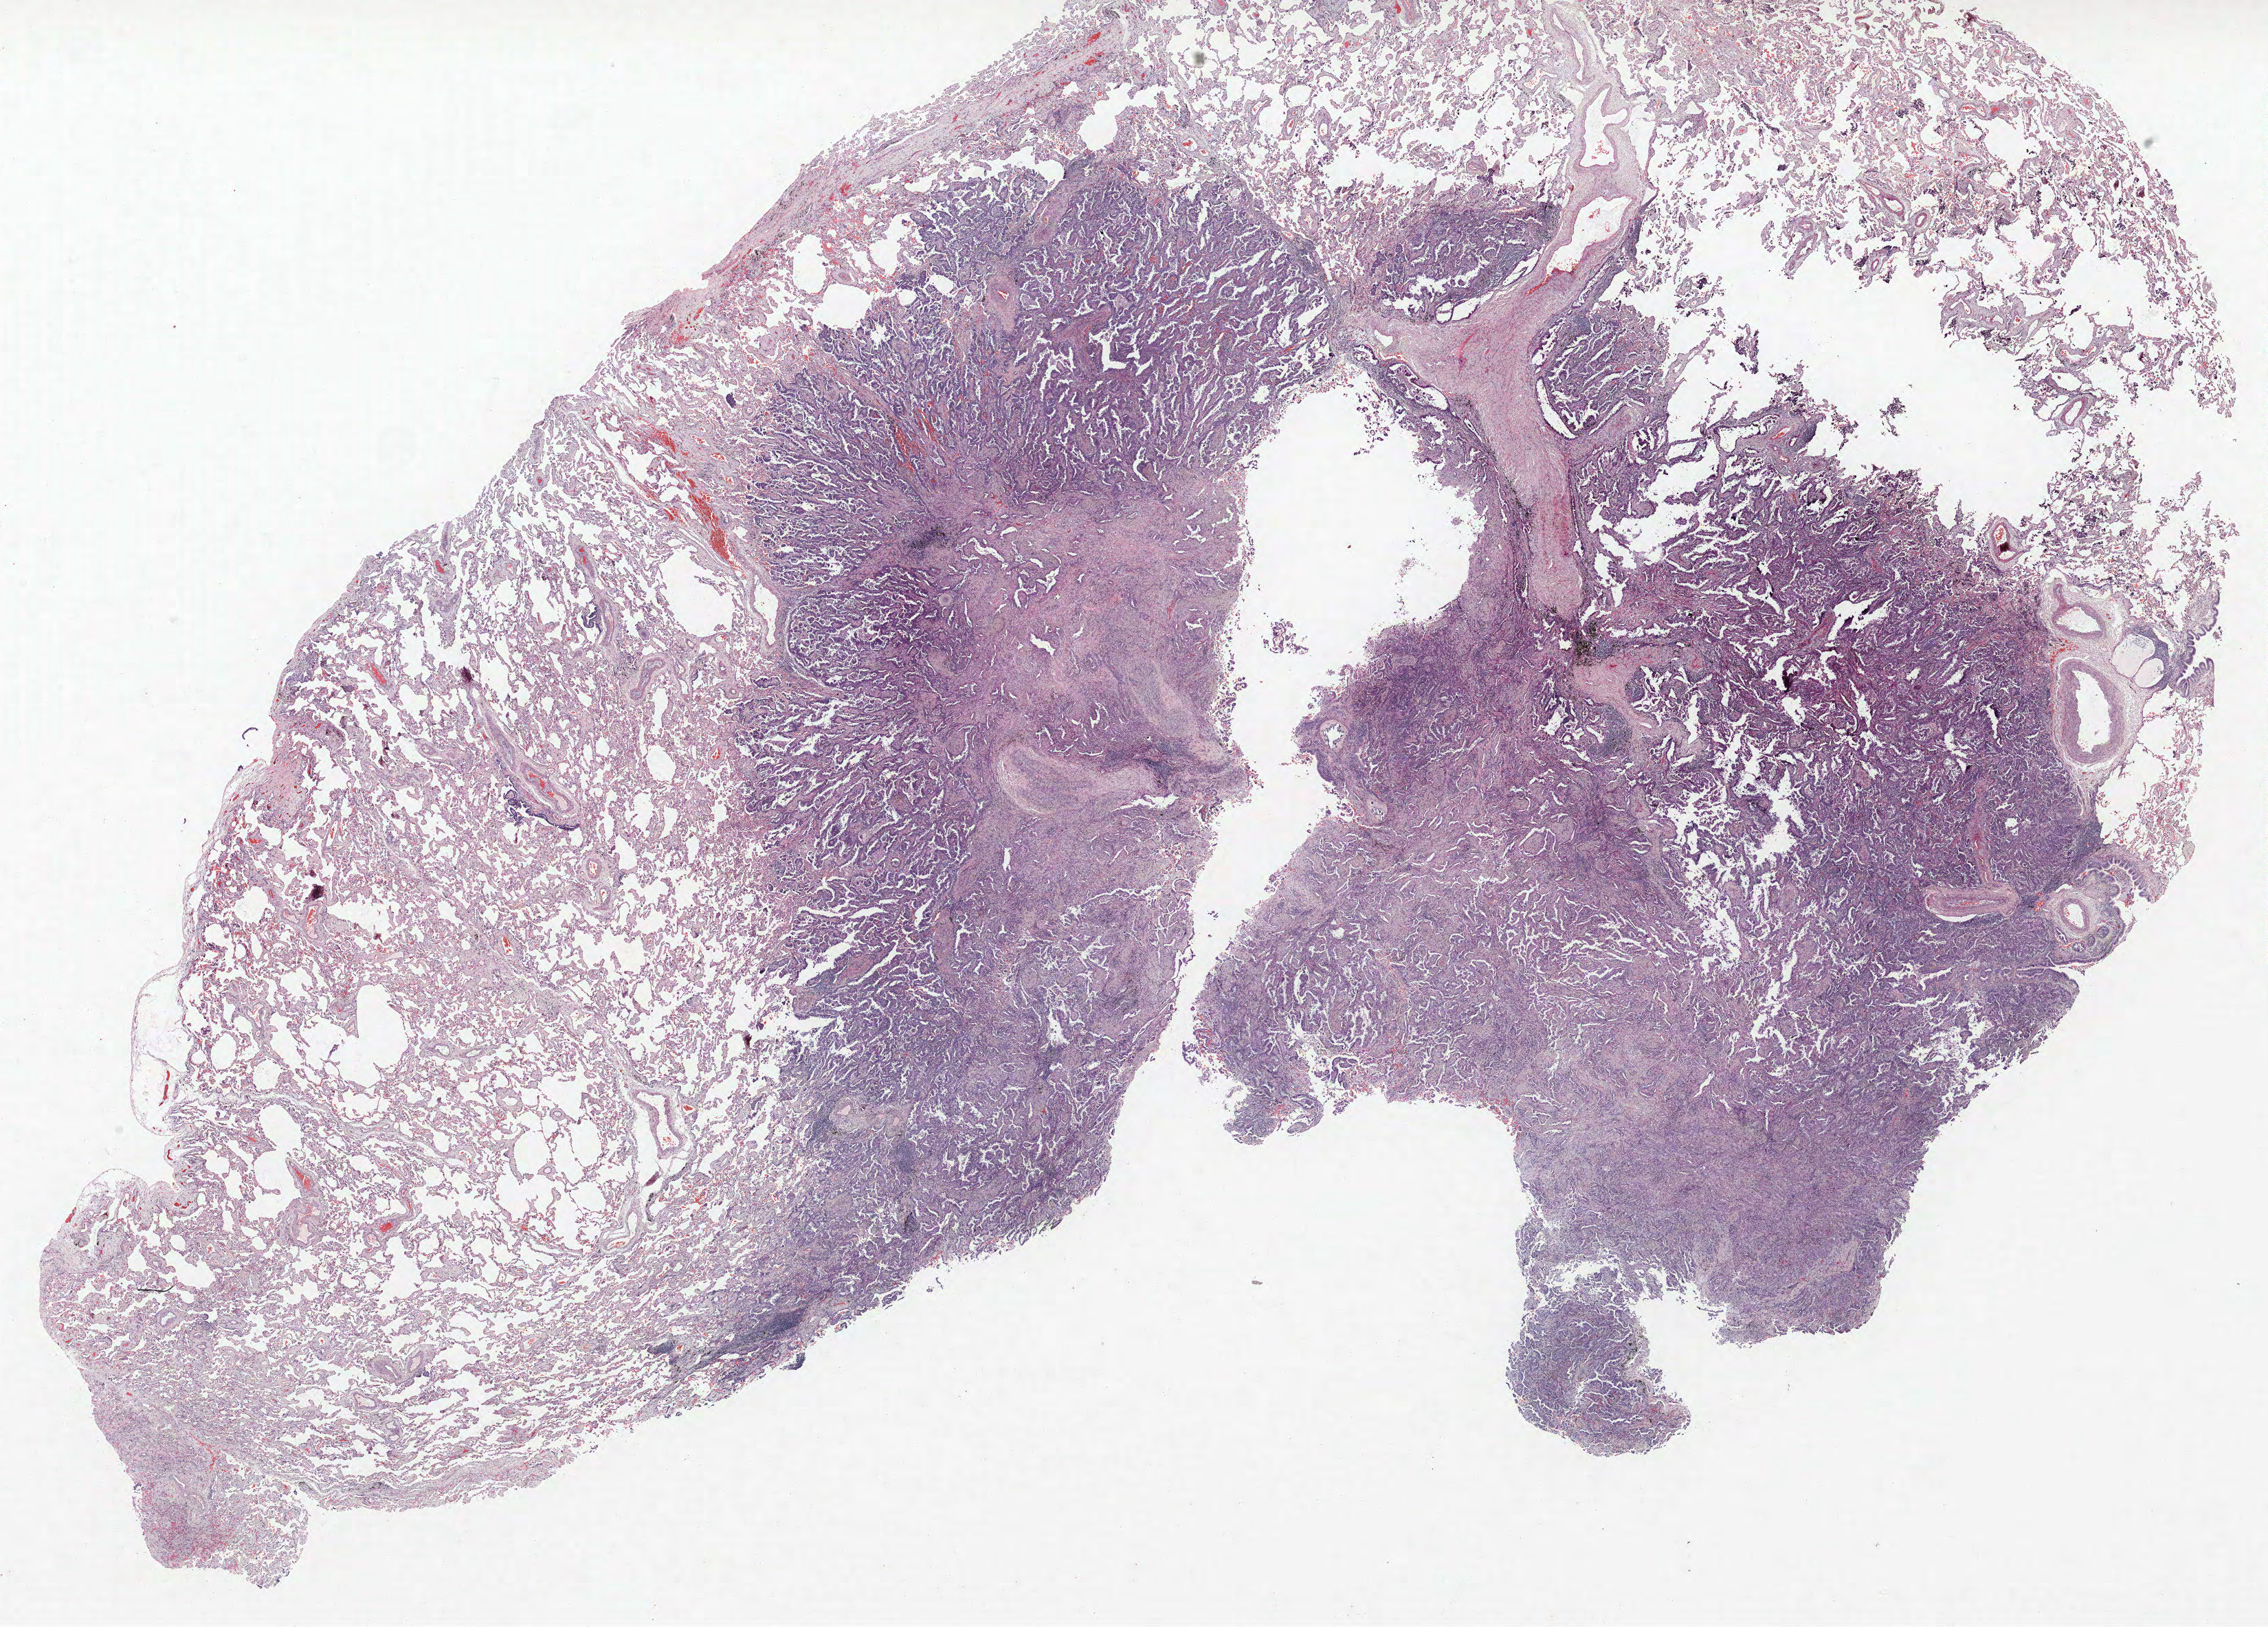
H&E-stained whole-slide image — shown as a low-resolution overview of the whole scanned area (about 26.4 x 18.9 mm), formalin-fixed paraffin-embedded (FFPE) section, lung. Male patient, aged 60 at enrolment. Former smoker at enrolment.
- stage (AJCC 6th edition): IA
- primary tumour location (clinical record): right lower lobe
- participant's lung-cancer diagnosis: Neoplasm, malignant
- ICD-O-3 topography: lower lobe of lung (C34.3)
- tumour size (pathology): 20 mm